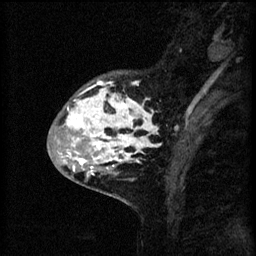
Breast MRI (dynamic contrast-enhanced), one sagittal slice; position 18 of 60 along the scan axis; 3 images stored at this slice position (order not interpretable as contrast timing); 1.5 T; TE 4.2 ms, TR 8.2 ms; 2 mm slice thickness; 256 × 256 image matrix, field of view 180 × 180 mm. Female patient, age 41 years.
Structures marked on this image (semi-automatically segmented with operator editing):
- analysis volume of interest (the breast-tissue region the enhancement analysis was run in; not a lesion): bounding box (x1, y1, x2, y2) in pixels: (53, 72, 159, 175)
- tumour enhancement mask (voxels above the 70 % enhancement threshold inside the analysis volume of interest): (65, 80, 159, 175)